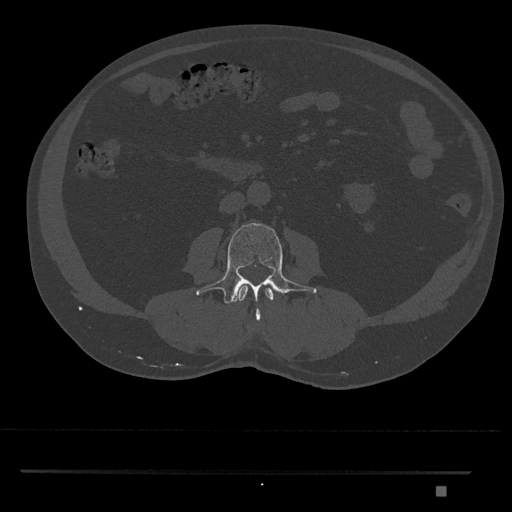
CT including the spine, one axial slice. Position 693 of 1134 along the scan axis. 120 kVp. Bone window (W 1800 / L 400 HU). 0.5 mm slice thickness. 512 × 512 image matrix, field of view 429 × 429 mm. Patient: male, 65 years. From the clinical record (not read from this slice): primary cancer: prostate.
Annotated regions visible in this slice (semi-automatic segmentation, software-assisted and operator-edited):
- L2 vertebra: bounding box (x1, y1, x2, y2) in pixels: (237, 286, 274, 302)
- L3 vertebra: (196, 223, 317, 321)